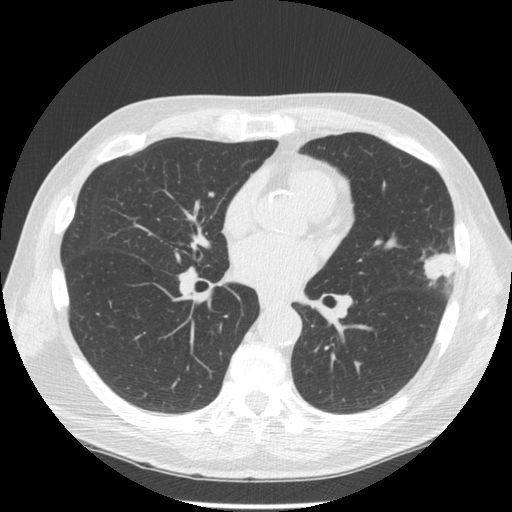
Low-dose screening chest CT, one axial slice. Position 70 of 134 along the scan axis. Reconstruction kernel STANDARD. Lung window (W 1500 / L -600 HU). 2.5 mm slice thickness. 512 × 512 image matrix, field of view 350 × 350 mm.
Outlined on this slice (expert manual segmentation):
- lesion 1 (tumor, upper lobe of left lung): bounding box [x1, y1, x2, y2] px = [424, 251, 456, 281]